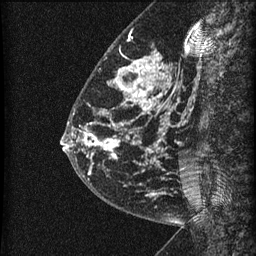
Breast MRI (dynamic contrast-enhanced), one sagittal slice; slice 19 of 60 in the series (ordered by position); dynamic contrast-enhanced series, image 2 of 3 at this slice position (ordered by acquisition); 1.5 T; TE 4.2 ms, TR 22.7 ms; 1.5 mm slice thickness; 256 × 256 image matrix, field of view 180 × 180 mm. Patient: female, 48 years. From the clinical record (not read from this slice): setting: breast cancer imaged before/during neoadjuvant chemotherapy; receptor status: triple-negative.
Annotated regions visible in this slice (semi-automatically segmented with operator editing):
- analysis volume of interest (the breast-tissue region the enhancement analysis was run in; not a lesion): bounding box <81,23,186,202> (left, top, right, bottom; pixels)
- tumour enhancement mask (voxels above the 90 % enhancement threshold inside the analysis volume of interest): <83,57,164,196>